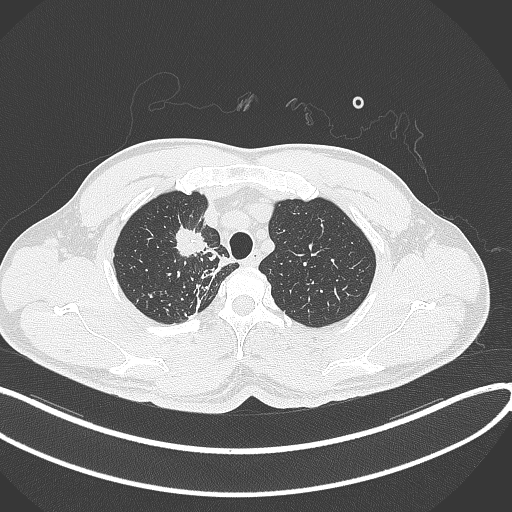
Chest CT, one axial slice; slice 315 of 391 in the series (ordered by position); reconstruction kernel B70f; 120 kVp; lung window (W 1500 / L -600 HU); 1 mm slice thickness; 512 × 512 image matrix, field of view 400 × 400 mm. Patient: male, 48 years. From the clinical record (not read from this slice): clinical TNM (as recorded): T1c N1 M1.
Outlined on this slice (bounding box drawn by a radiologist):
- lung tumour (recorded histology: adenocarcinoma): box from (x=170, y=222) to (x=208, y=257) px